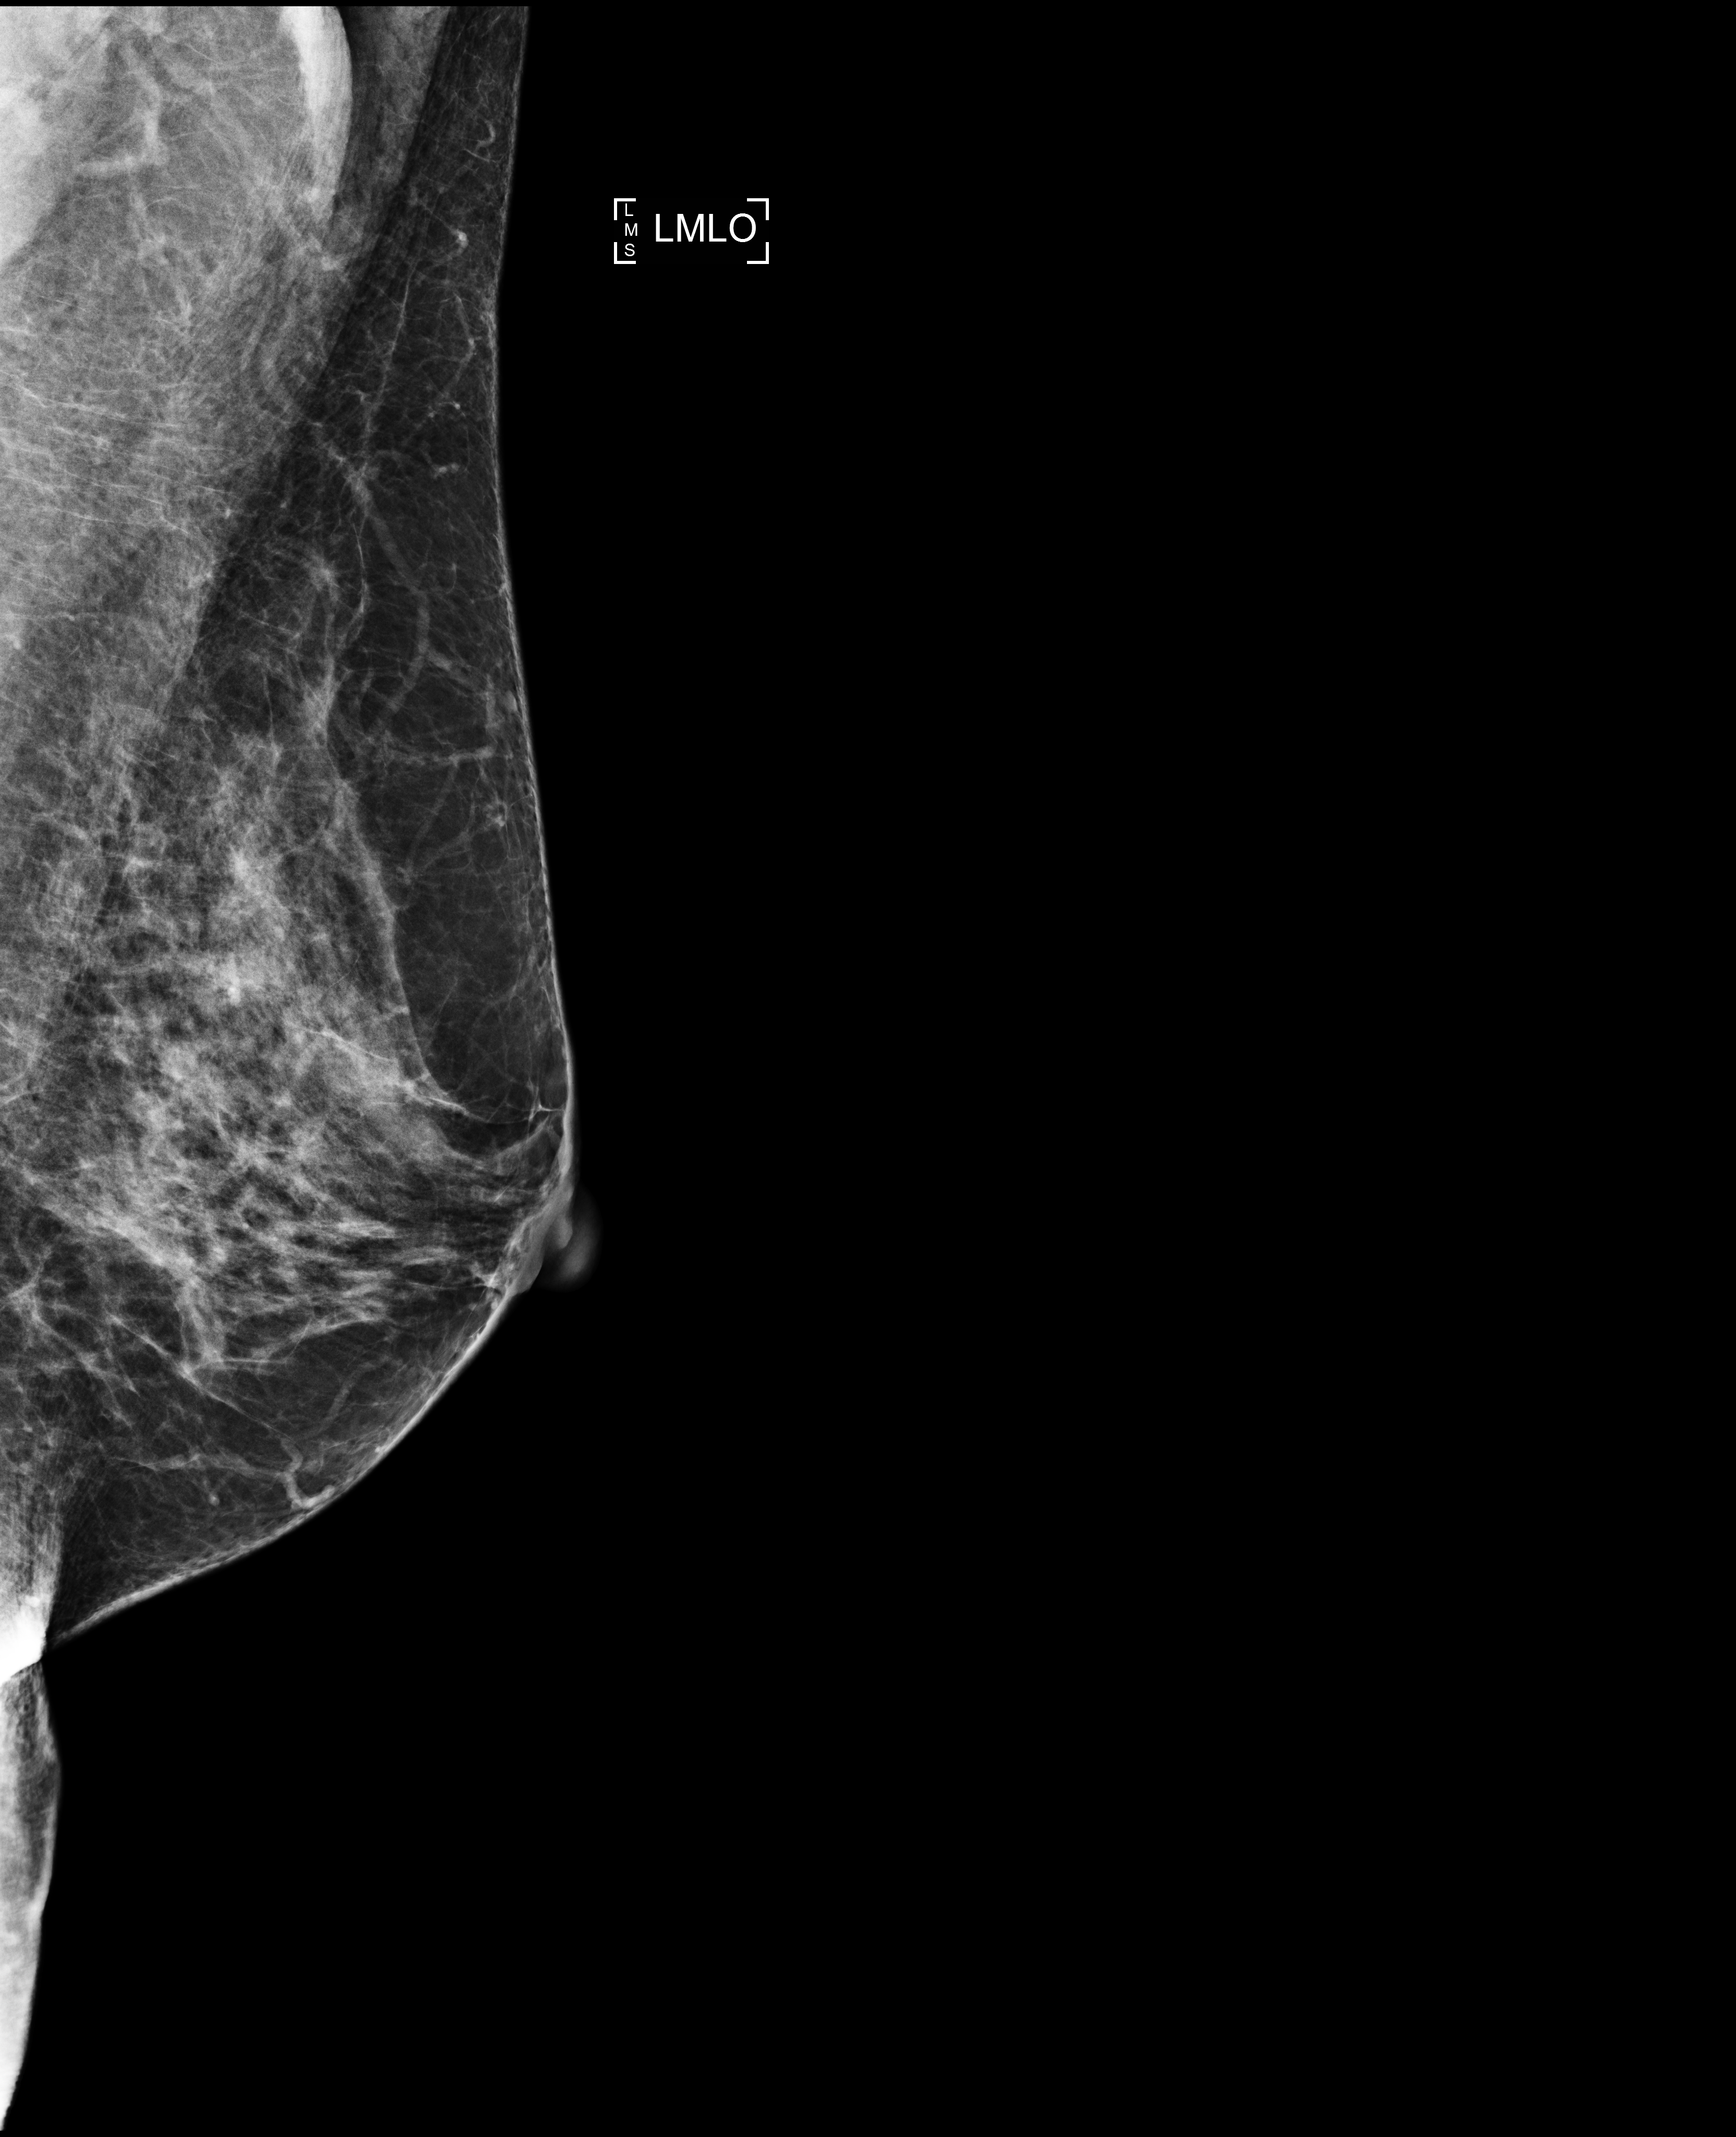
Full-field digital mammogram (FFDM); left breast; MLO view; screening examination; compressed breast thickness 60 mm. Female patient, age 59 years.
BI-RADS breast density category at the screening exam (both breasts, scale 1–4): 3. Final BI-RADS category for the screening round (tomosynthesis exam, both breasts): category 1. Recall: no recall after this screen.